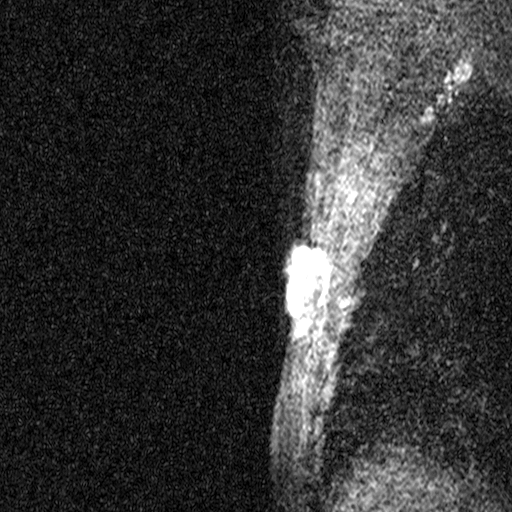
Breast MRI (dynamic contrast-enhanced), one sagittal slice; slice 34 of 44 in the series (ordered by position); dynamic contrast-enhanced study with each time point stored as its own series, time point 2 of 3 at this slice position (early post-contrast, ordered by acquisition time); 1.5 T; TE 4.5 ms, TR 11 ms; 512 × 512 image matrix, field of view 200 × 200 mm. Female patient, age 45 years. From the clinical record (not read from this slice): setting: breast cancer imaged before/during neoadjuvant chemotherapy; receptor status: HR-positive, HER2-negative.
Structures marked on this image (semi-automatic segmentation, software-assisted and operator-edited):
- analysis volume of interest (the breast-tissue region the enhancement analysis was run in; not a lesion): bounding box [x1, y1, x2, y2] px = [256, 218, 333, 359]
- tumour enhancement mask (voxels above the 90 % enhancement threshold inside the analysis volume of interest): [286, 250, 328, 310]